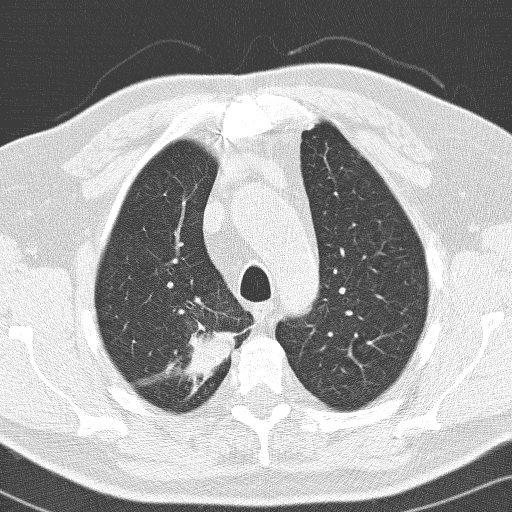
Low-dose screening chest CT, one axial slice; position 113 of 141 along the scan axis; lung window (W 1500 / L -600 HU); 3.2 mm slice thickness; 512 × 512 image matrix, field of view 326 × 326 mm.
Structures marked on this image (outlined manually by an expert reader):
- lesion 1 (tumor, upper lobe of right lung): box from (x=186, y=321) to (x=239, y=394) px